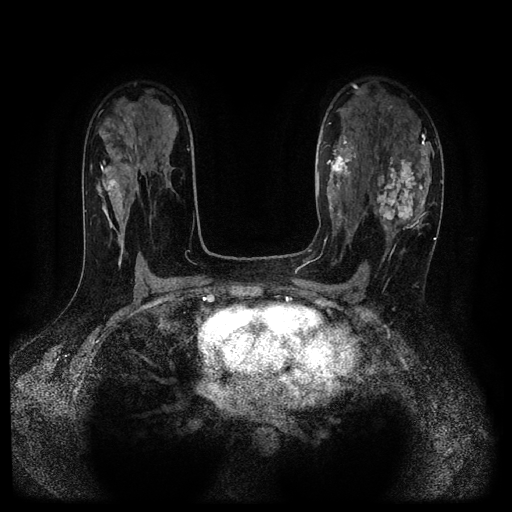
Breast MRI (dynamic contrast-enhanced, multi-phase), one axial slice; dynamic contrast-enhanced series, time point 2 of 5 at this slice position (early post-contrast); 1.5 T; TE 2.7 ms, TR 5.4 ms; 2.2 mm slice thickness; 512 × 512 image matrix, field of view 330 × 330 mm. Female patient, age 43 years.
Annotated regions visible in this slice (semi-automatically segmented with operator editing):
- breast lesion (labelled 'tumour' in the annotation; benign lesions carry a separate 'benign' label): bounding box [x1, y1, x2, y2] px = [369, 152, 429, 235]
- breast lesion (labelled benign in the annotation): [326, 136, 356, 198]